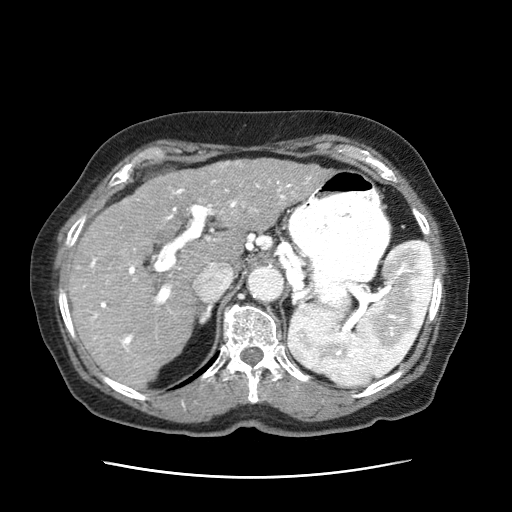
Contrast-enhanced abdominal CT (liver protocol), one axial slice; 120 kVp; intravenous contrast given; soft-tissue window (W 400 / L 40 HU); 2.5 mm slice thickness; 512 × 512 image matrix, field of view 360 × 360 mm. Patient: female, 79 years. From the clinical record (not read from this slice): diagnosis: hepatocellular carcinoma (patient treated with transarterial chemoembolisation; whether this scan precedes or follows treatment is not stated here); TNM stage (as recorded): Stage-II.
Structures marked on this image (semi-automatically segmented with operator editing):
- abdominal aorta: bounding box [x1, y1, x2, y2] px = [247, 267, 283, 301]
- liver parenchyma outside the tumour (the mass and vessels are separate outlines, so this box may not span the whole liver): [66, 171, 251, 389]
- mass: [173, 159, 329, 229]
- liver vessels: [83, 181, 293, 352]